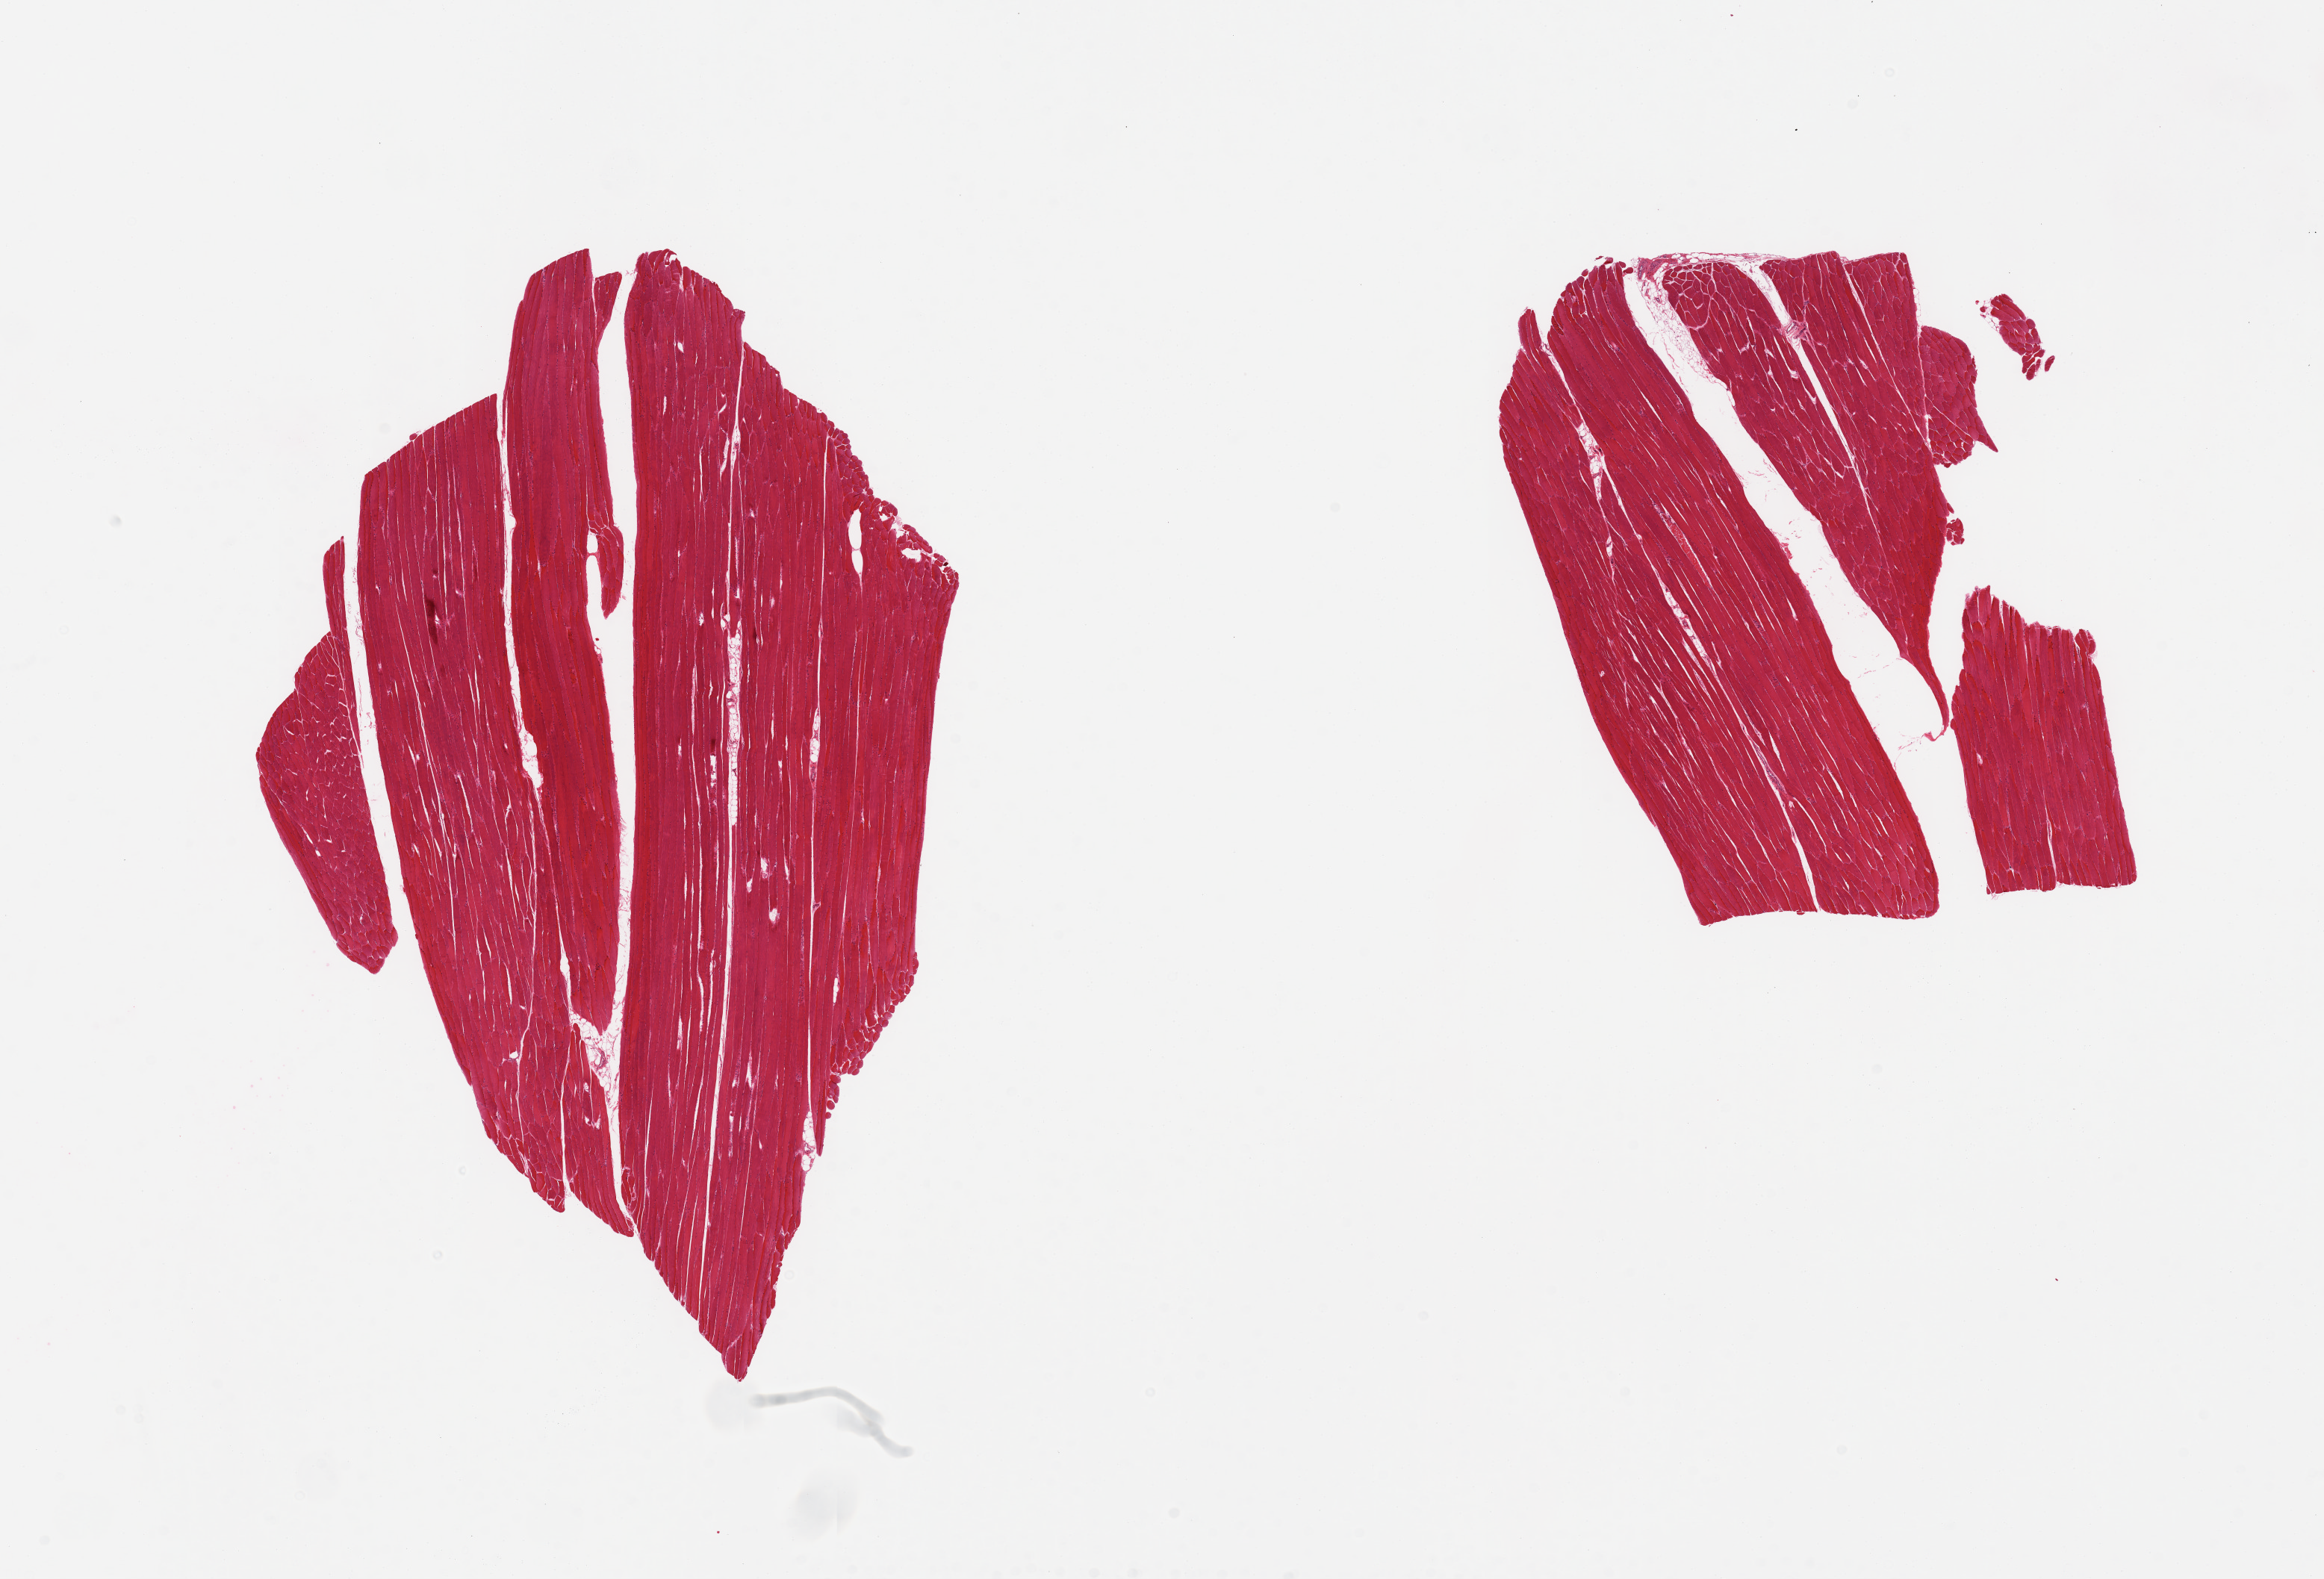
Whole-slide image, H&E stain, brightfield — whole scanned area (about 24.6 x 16.7 mm) shown as a low-resolution overview, PAXgene-fixed, paraffin-embedded tissue, section of skeletal muscle (target tissue), tissue donor sample.
Review note (as recorded): 2 pieces.